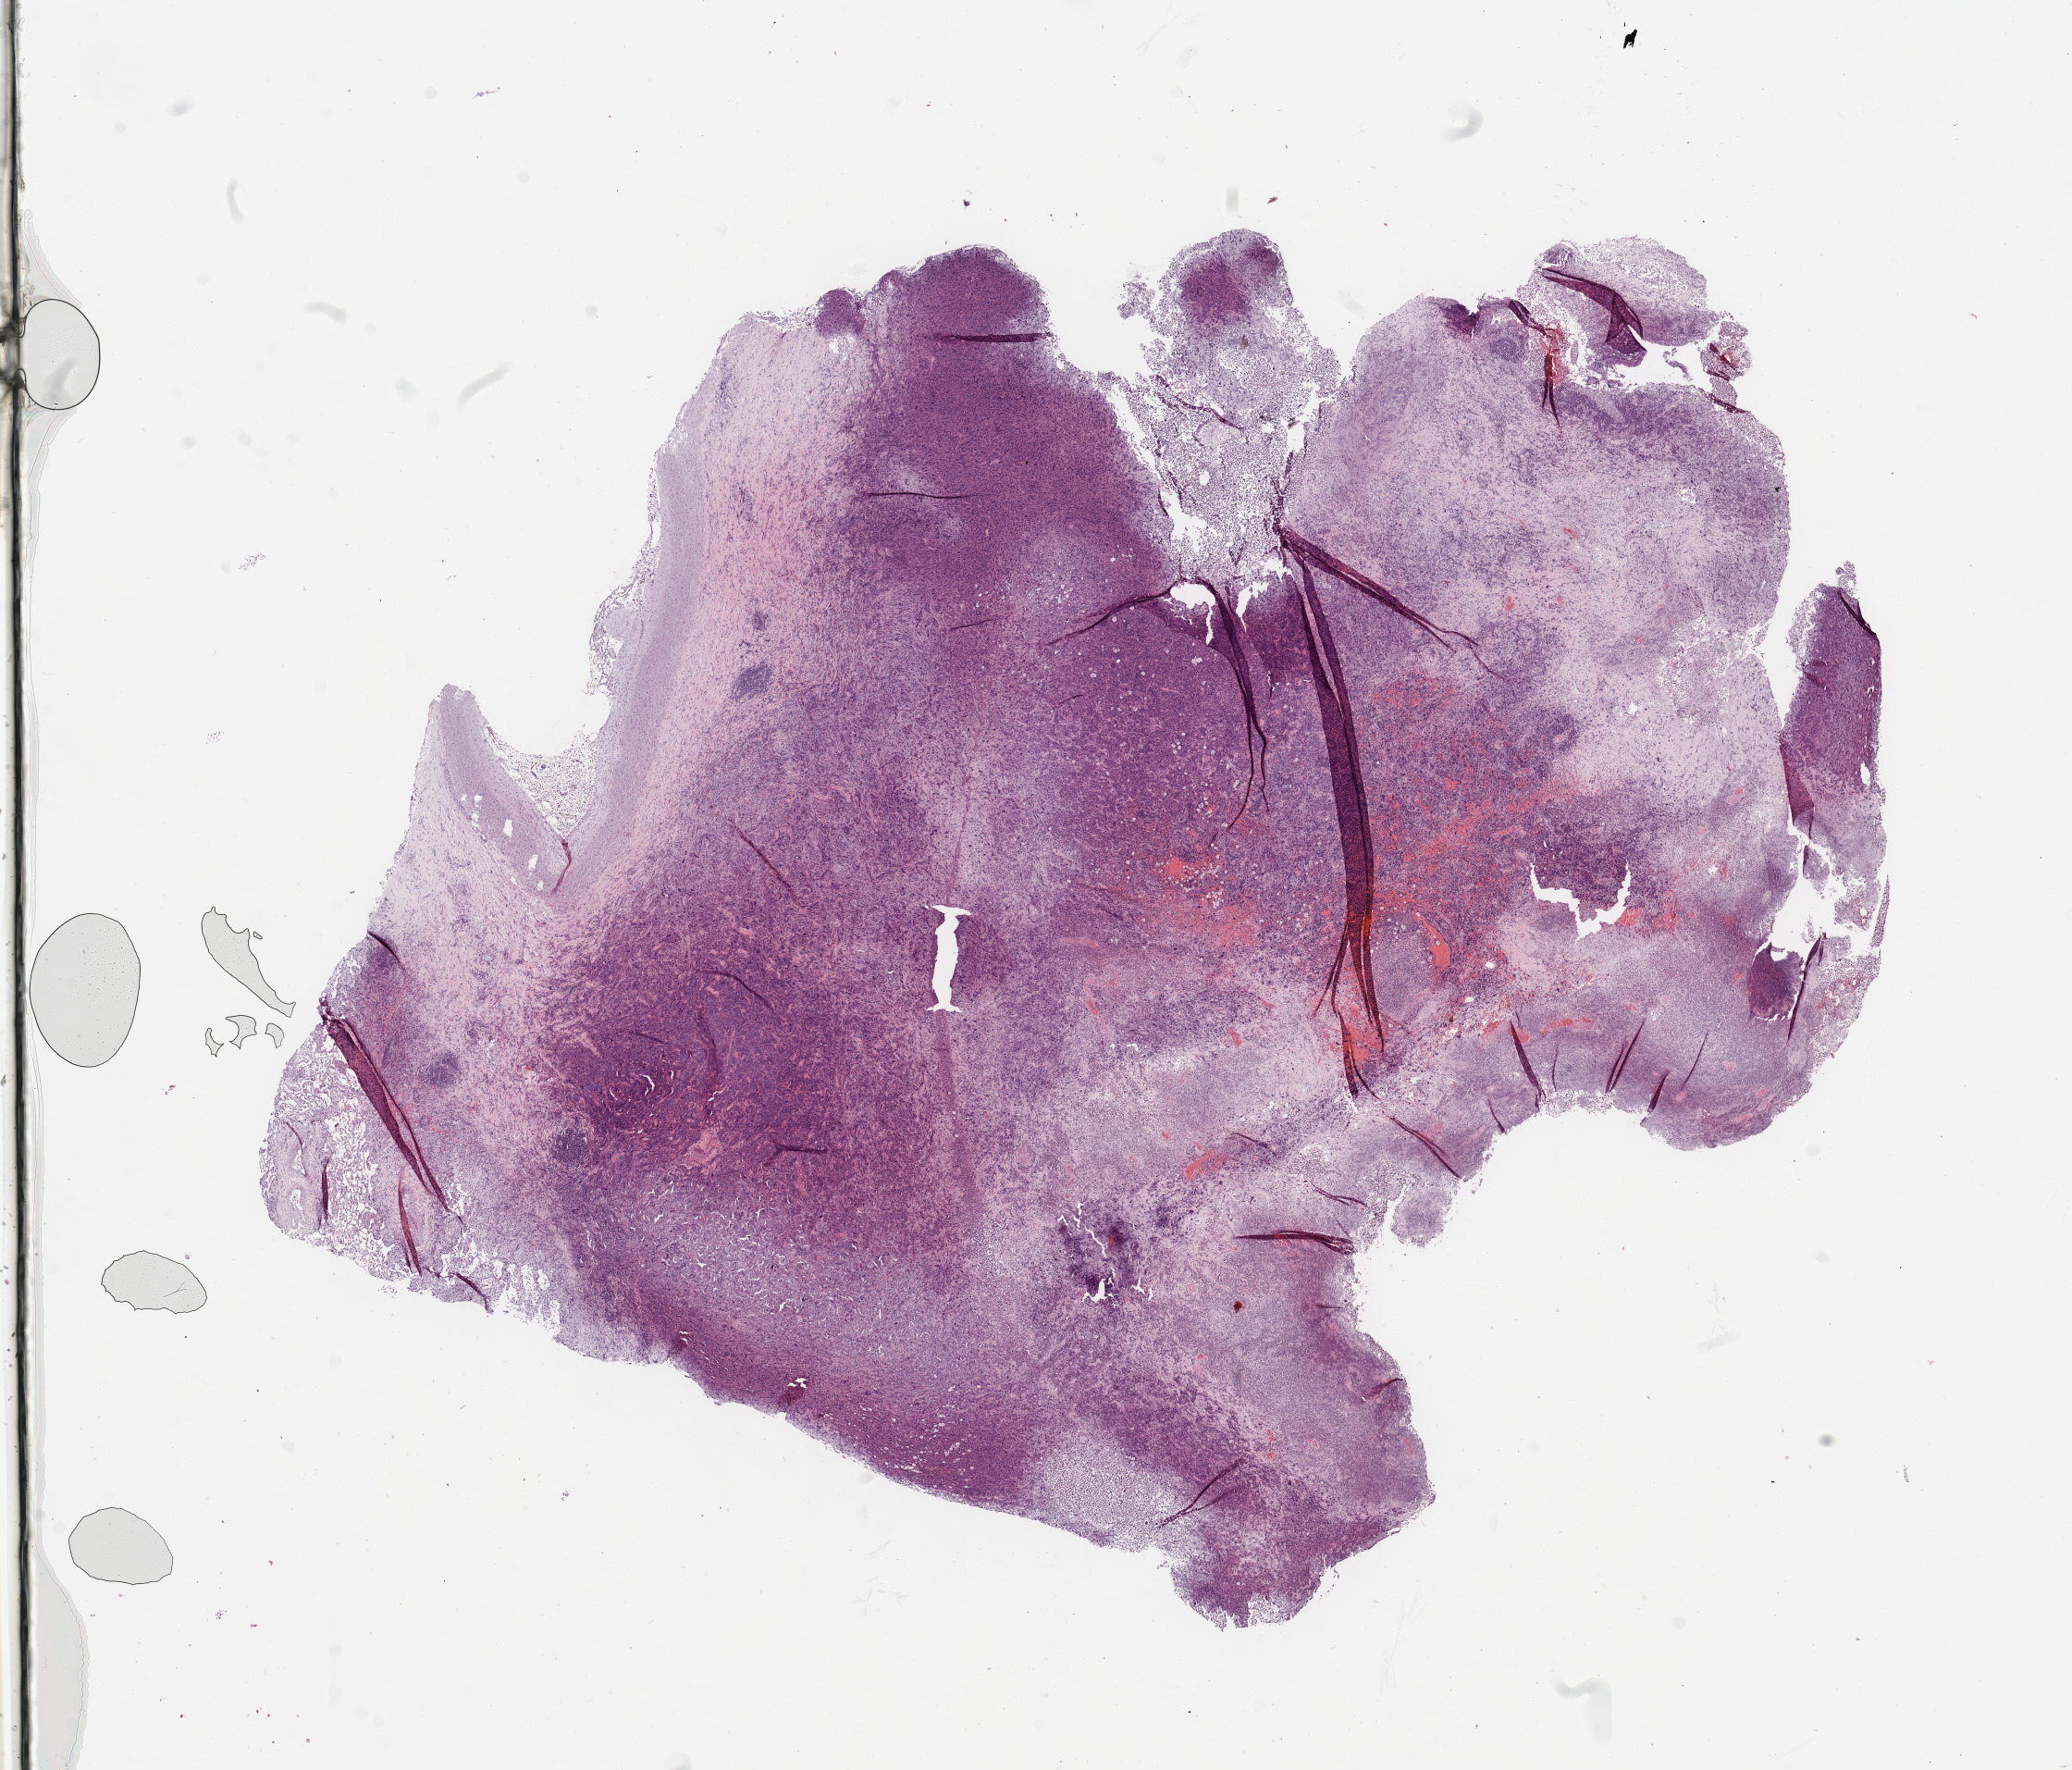
Whole-slide histology image, H&E-stained — whole scanned area (about 17.7 x 15.1 mm, from a 20x scan) shown as a low-resolution overview; lung, tumour tissue. Female, 70 y/o. Histologic grade: G3 (poorly differentiated).
Primary tumour site (as recorded): right lower lobe. Diagnosis: Squamous cell carcinoma, NOS.